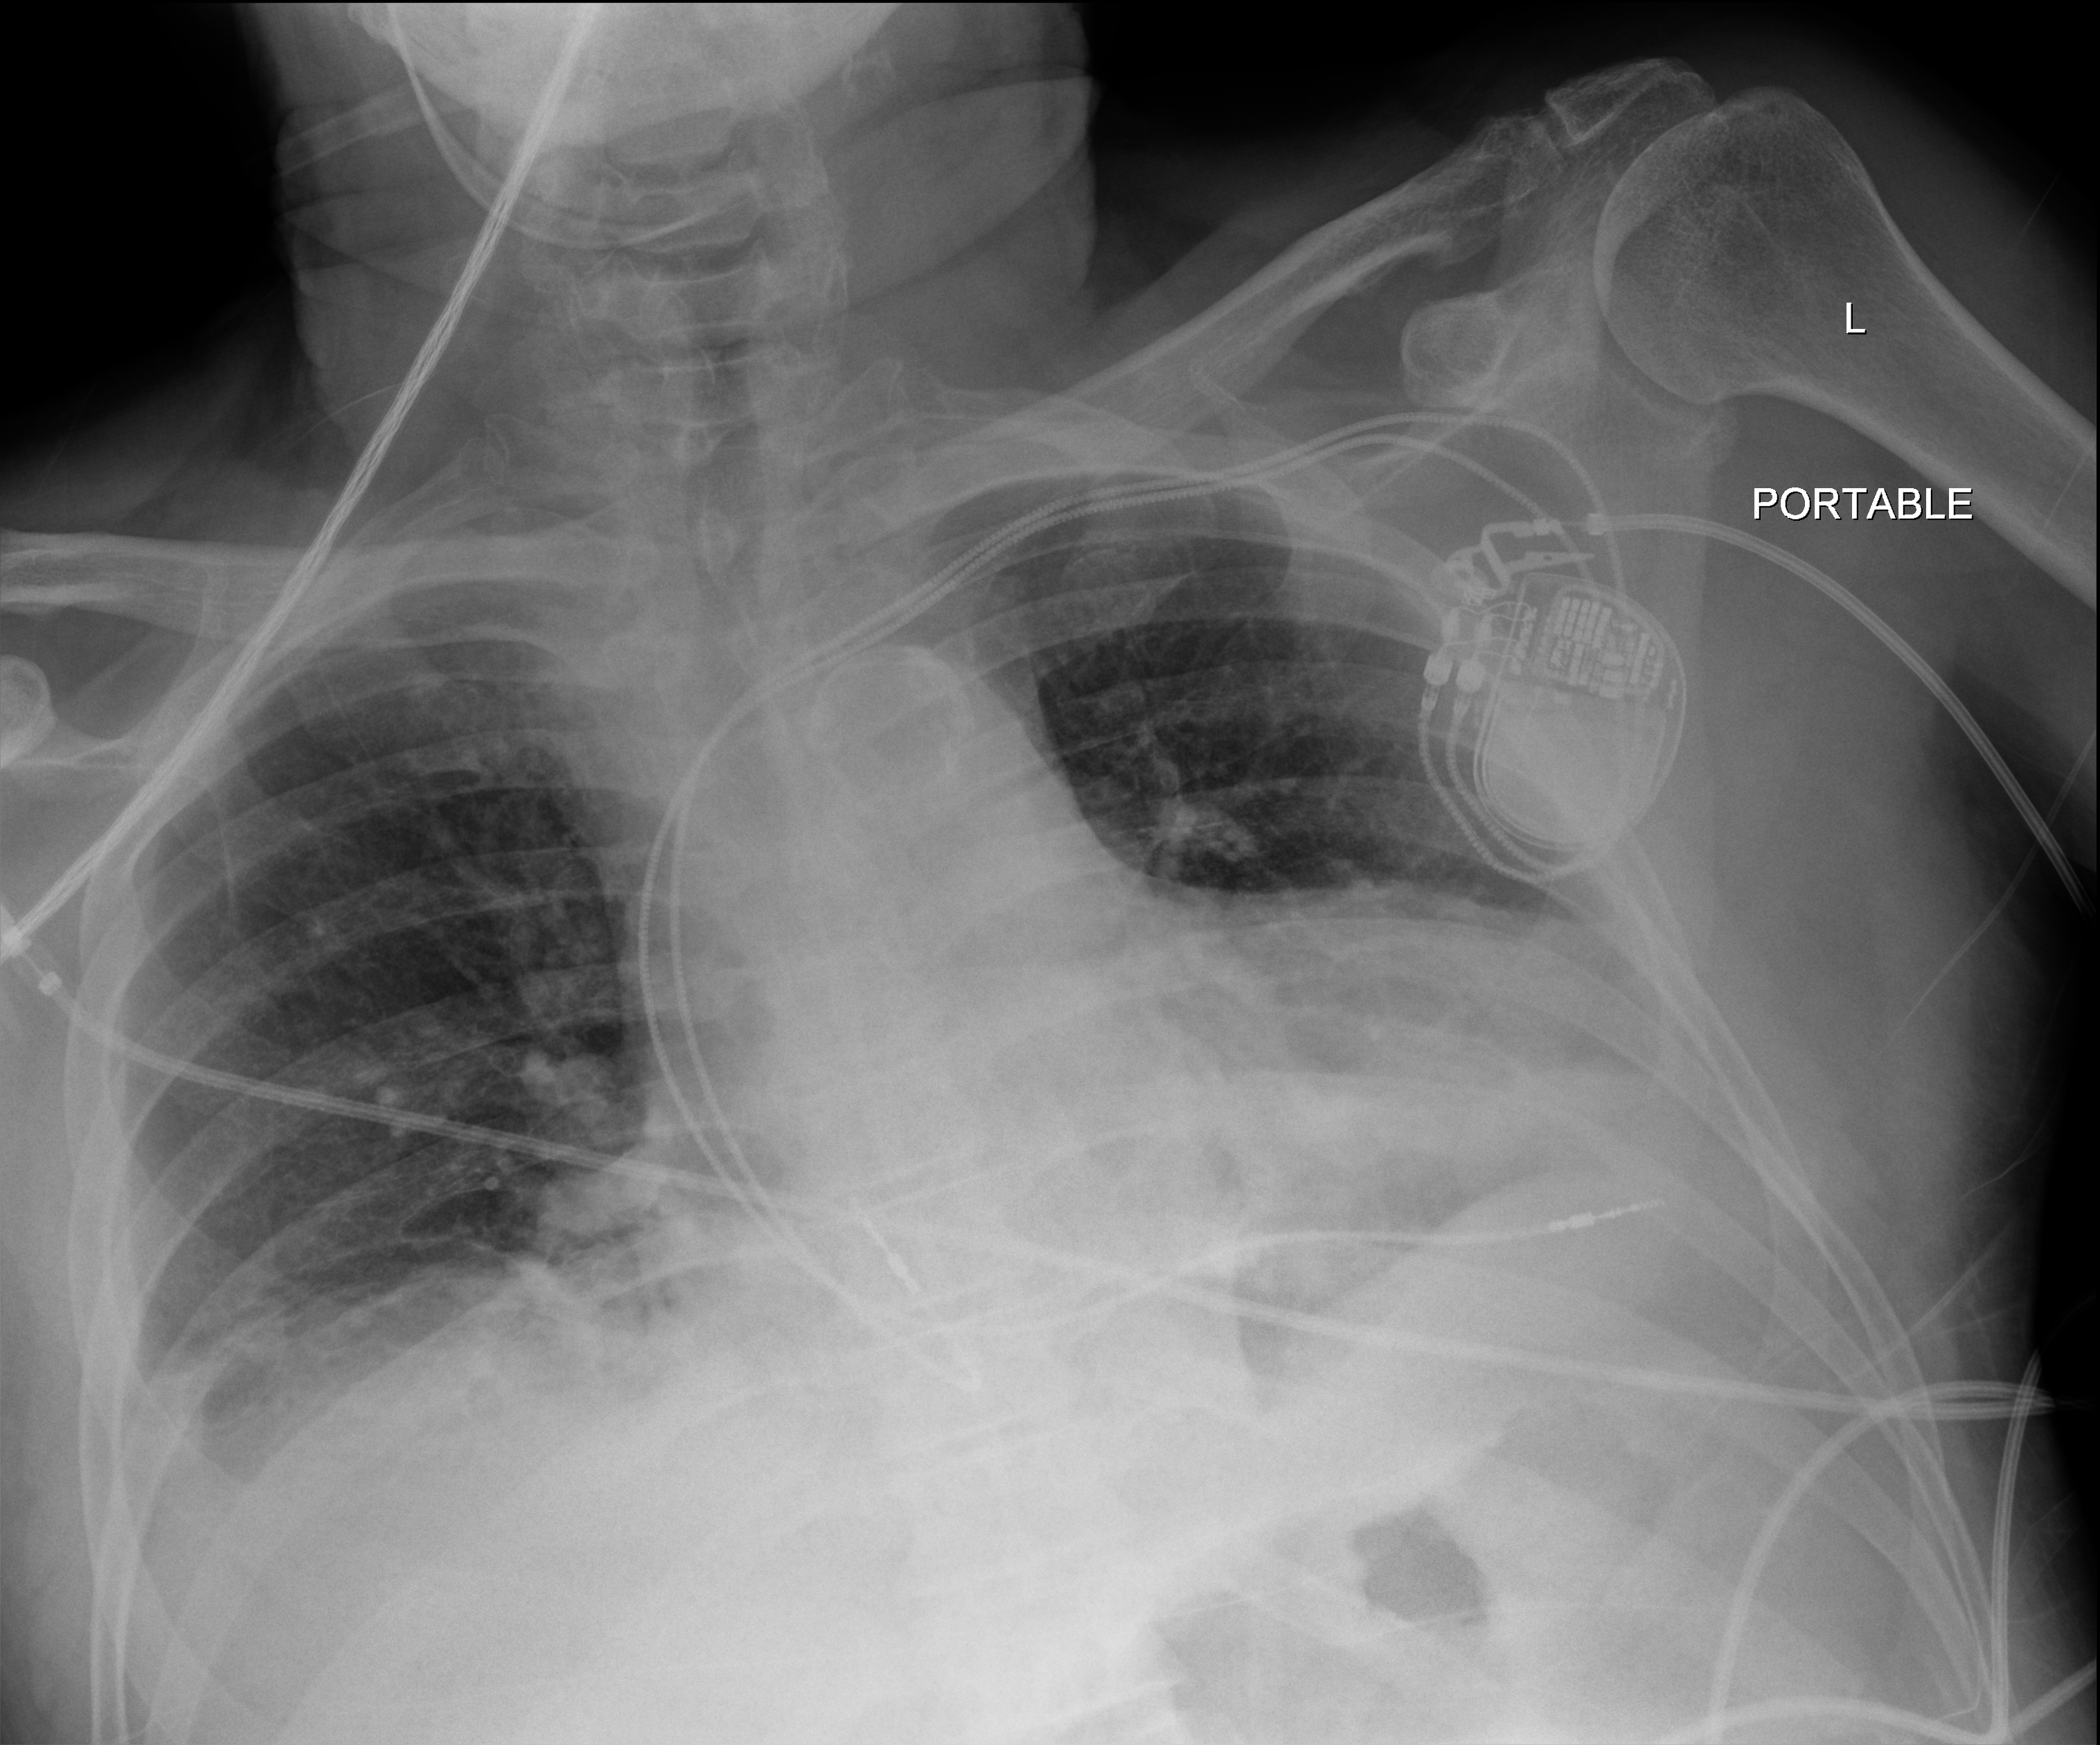
Bedside chest radiograph (digital radiography); anteroposterior (AP) projection. Male patient hospitalised with COVID-19, age 60–74 years.
Hospital-stay facts (about this admission, not read from this image; timing relative to this image not recorded): admitted to intensive care during this hospital stay: yes.